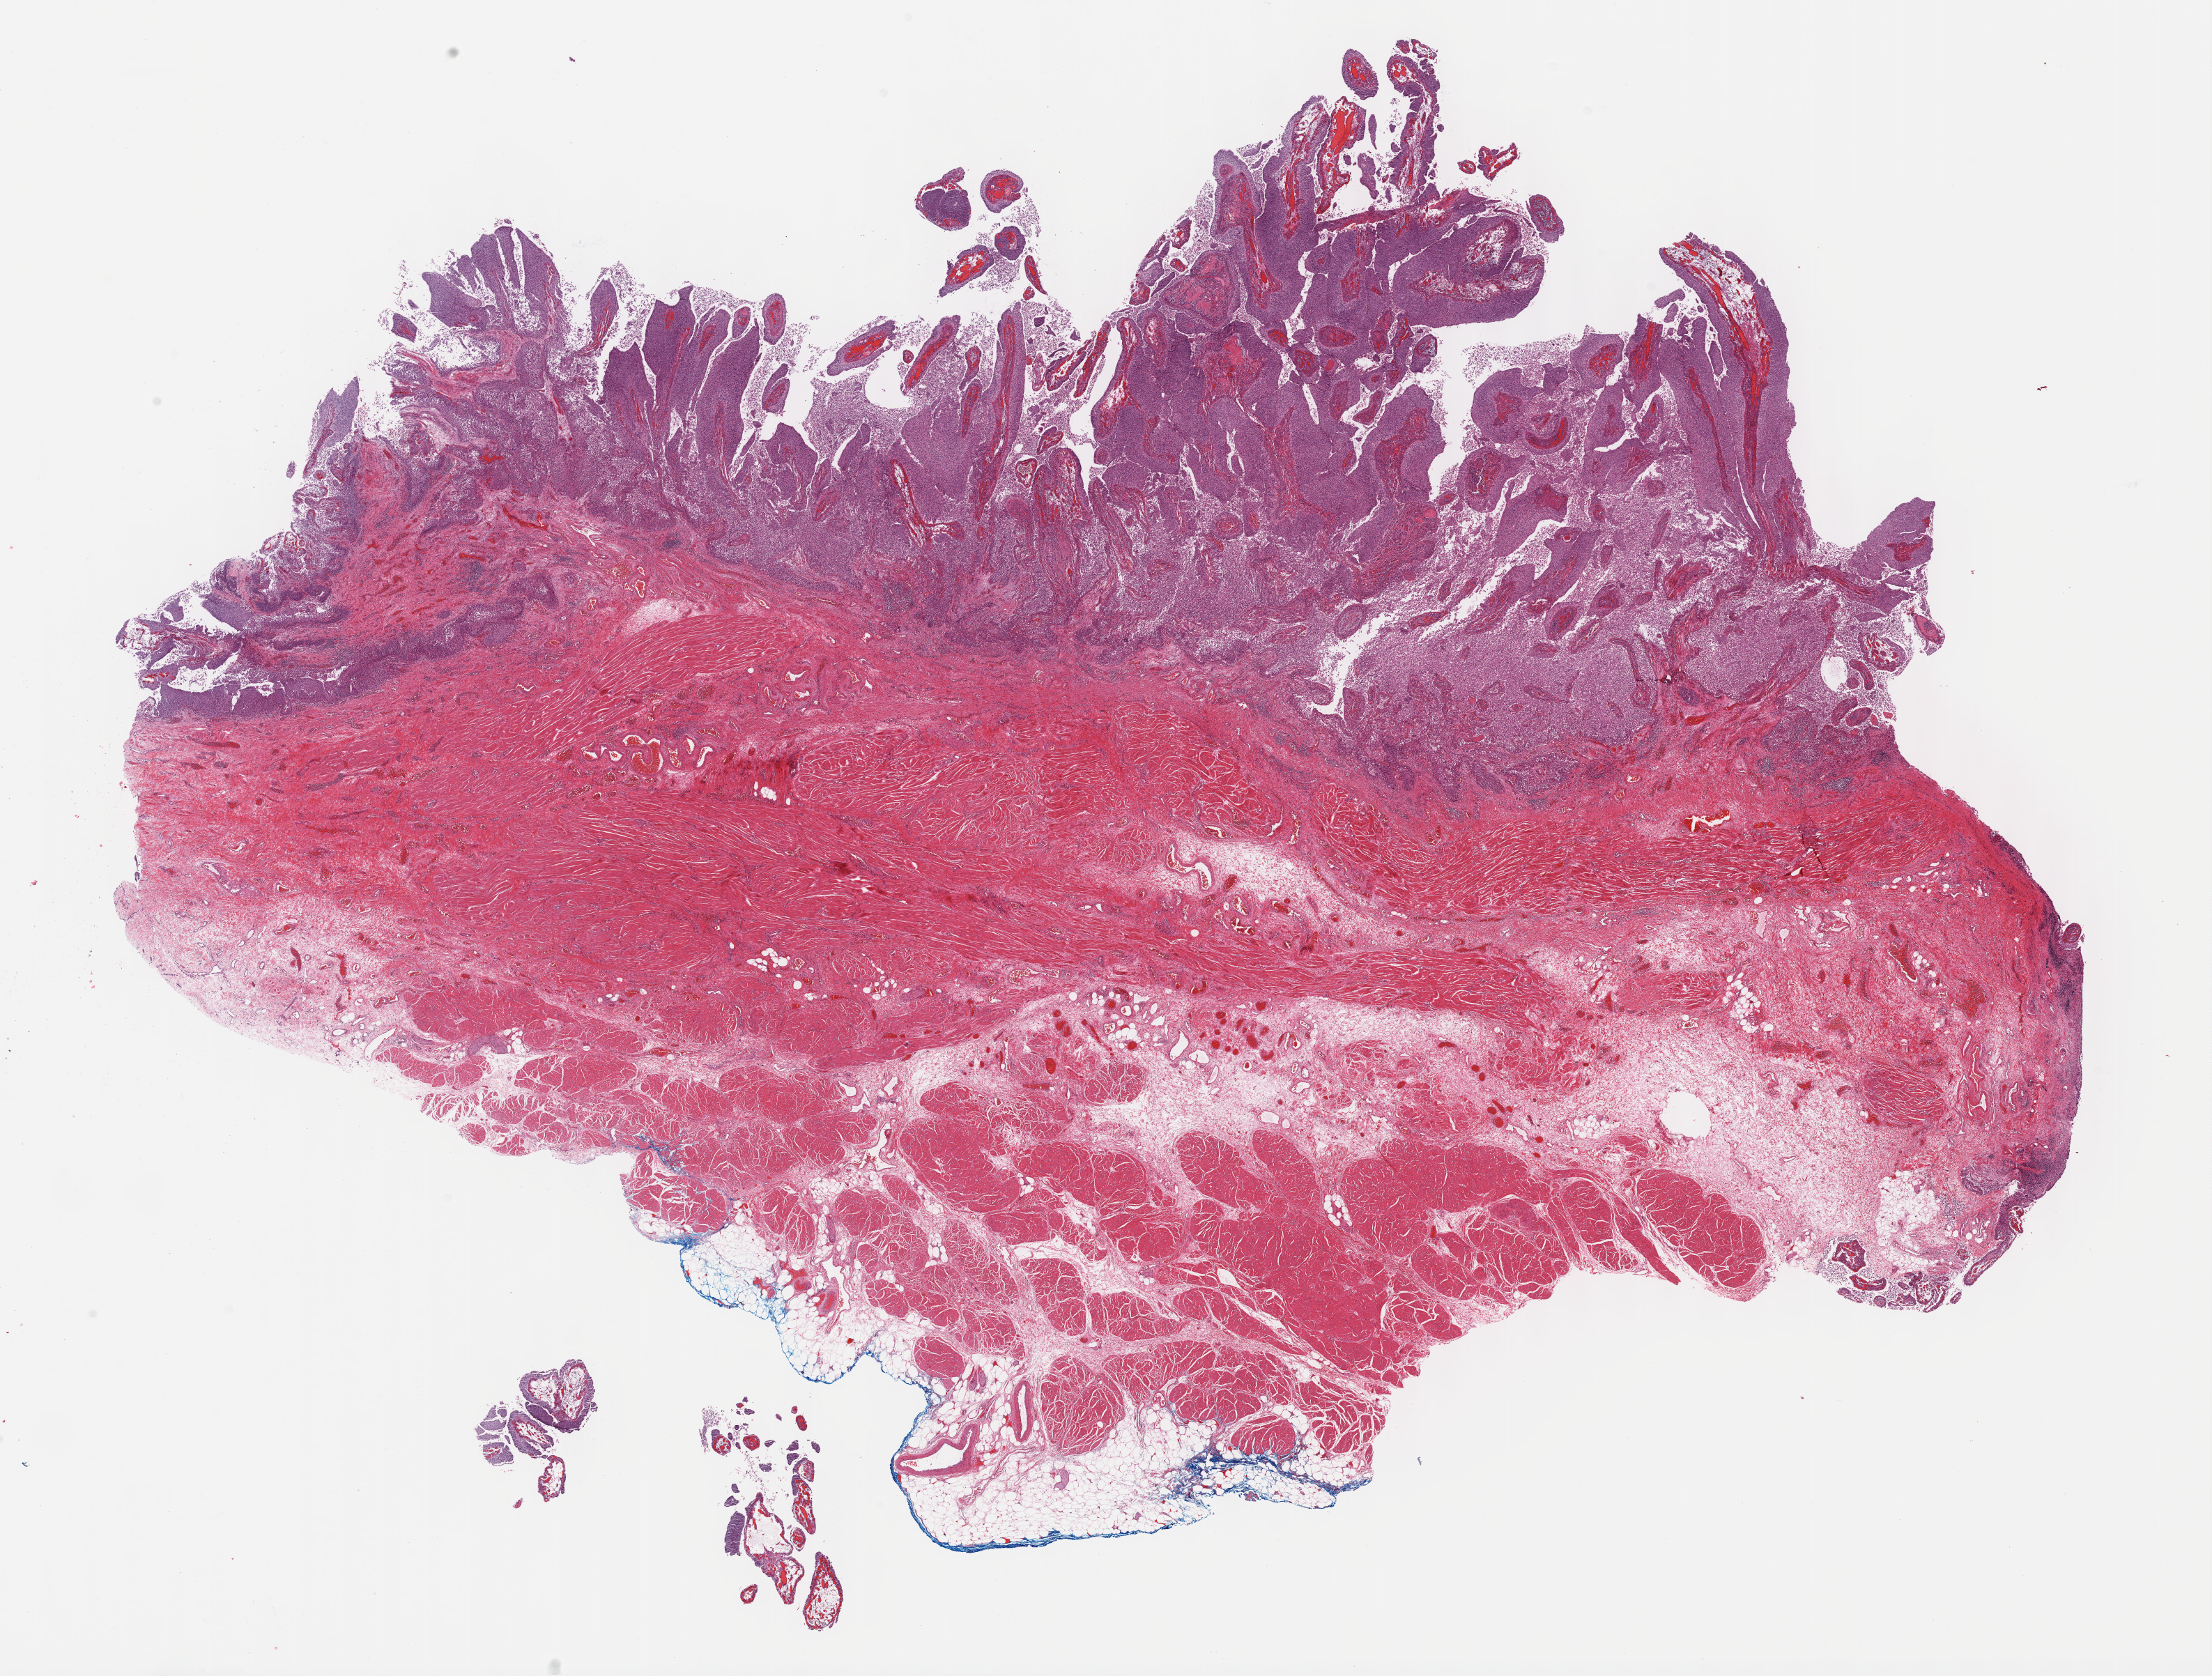
Digitized H&E-stained tissue section (whole slide) — shown as a low-resolution overview of the whole scanned area (about 25.7 x 19.5 mm), formalin-fixed paraffin-embedded (FFPE) diagnostic section, sample: primary tumour, bladder. Male, age 71 years at initial diagnosis. Histologic grade: high grade.
TNM: T2a N0 MX. AJCC pathologic stage: II (7th edition). Diagnosis: Papillary transitional cell carcinoma.